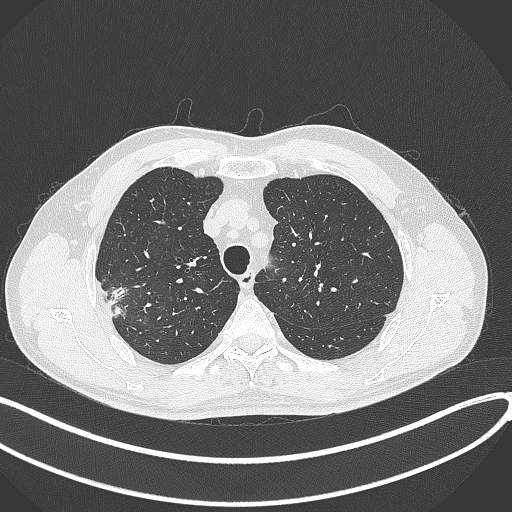
Chest CT, one axial slice. Position 330 of 381 along the scan axis. Reconstruction kernel B70f. Lung window (W 1500 / L -600 HU). 1 mm slice thickness. 512 × 512 image matrix, field of view 400 × 400 mm. Male patient, age 62 years. From the clinical record (not read from this slice): clinical TNM (as recorded): T1c N0 M0; histopathological grade: G2-3.
Annotated regions visible in this slice (bounding box drawn by a radiologist):
- lung tumour (recorded histology: adenocarcinoma): bounding box <105,282,133,321> (left, top, right, bottom; pixels)